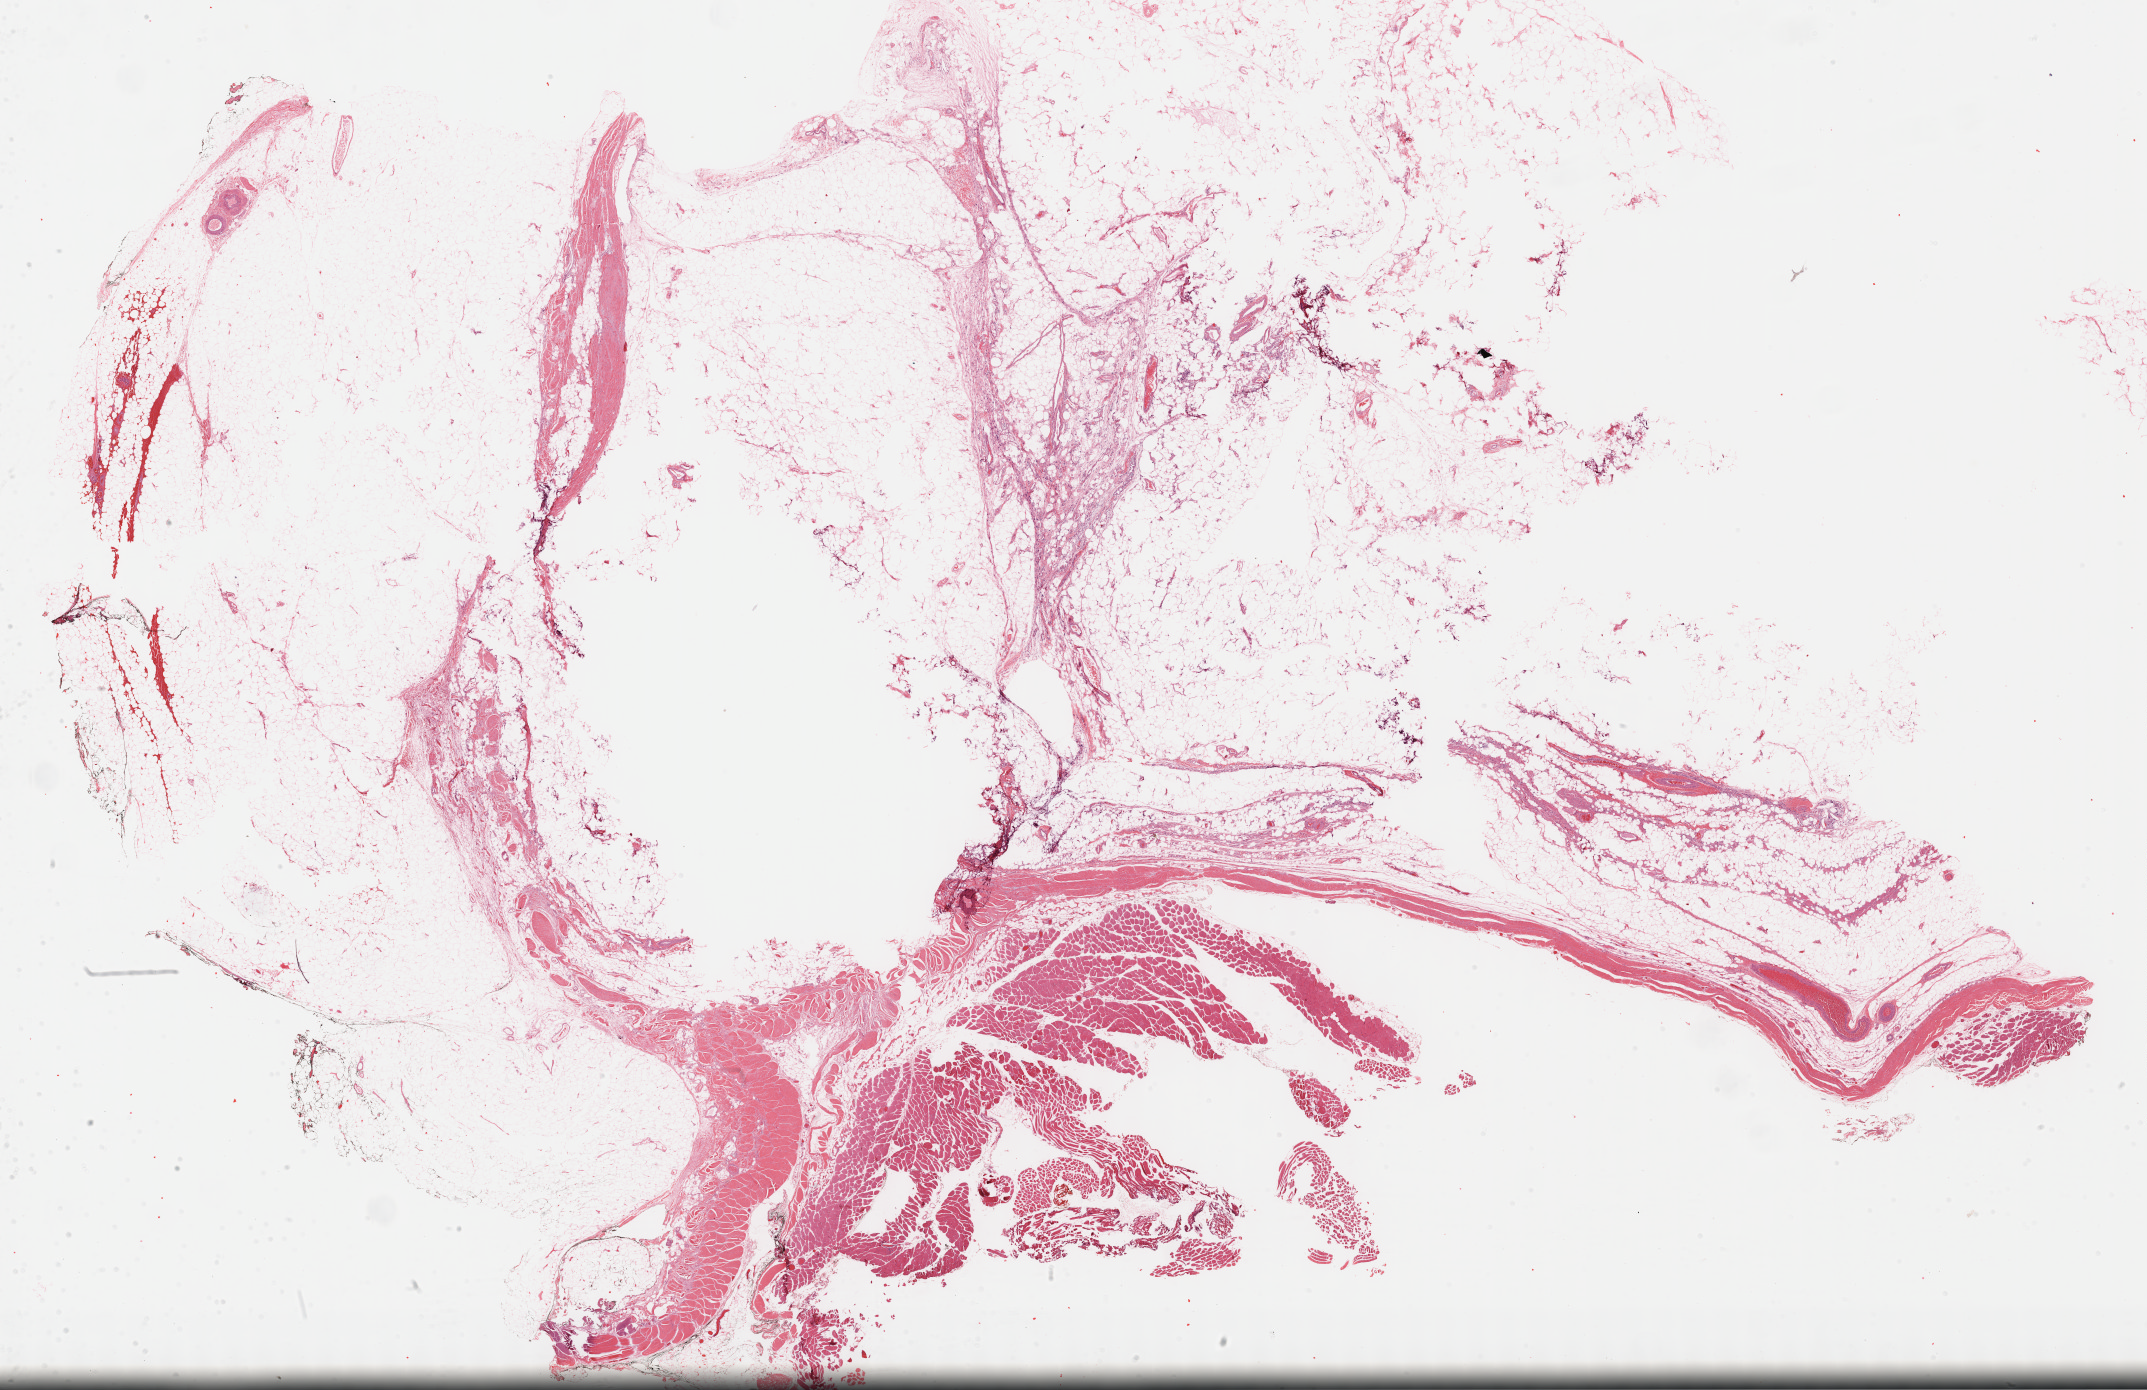
Whole-slide histology image, Hematoxylin and eosin (H&E) stained — low-resolution overview of the scanned area, about 34.7 x 22.5 mm, FFPE section, primary tumour sample from the connective, subcutaneous and other soft tissues. Patient: female, age at initial diagnosis 73 years.
* pathologic diagnosis: Dedifferentiated liposarcoma (connective, subcutaneous and other soft tissues of lower limb and hip)